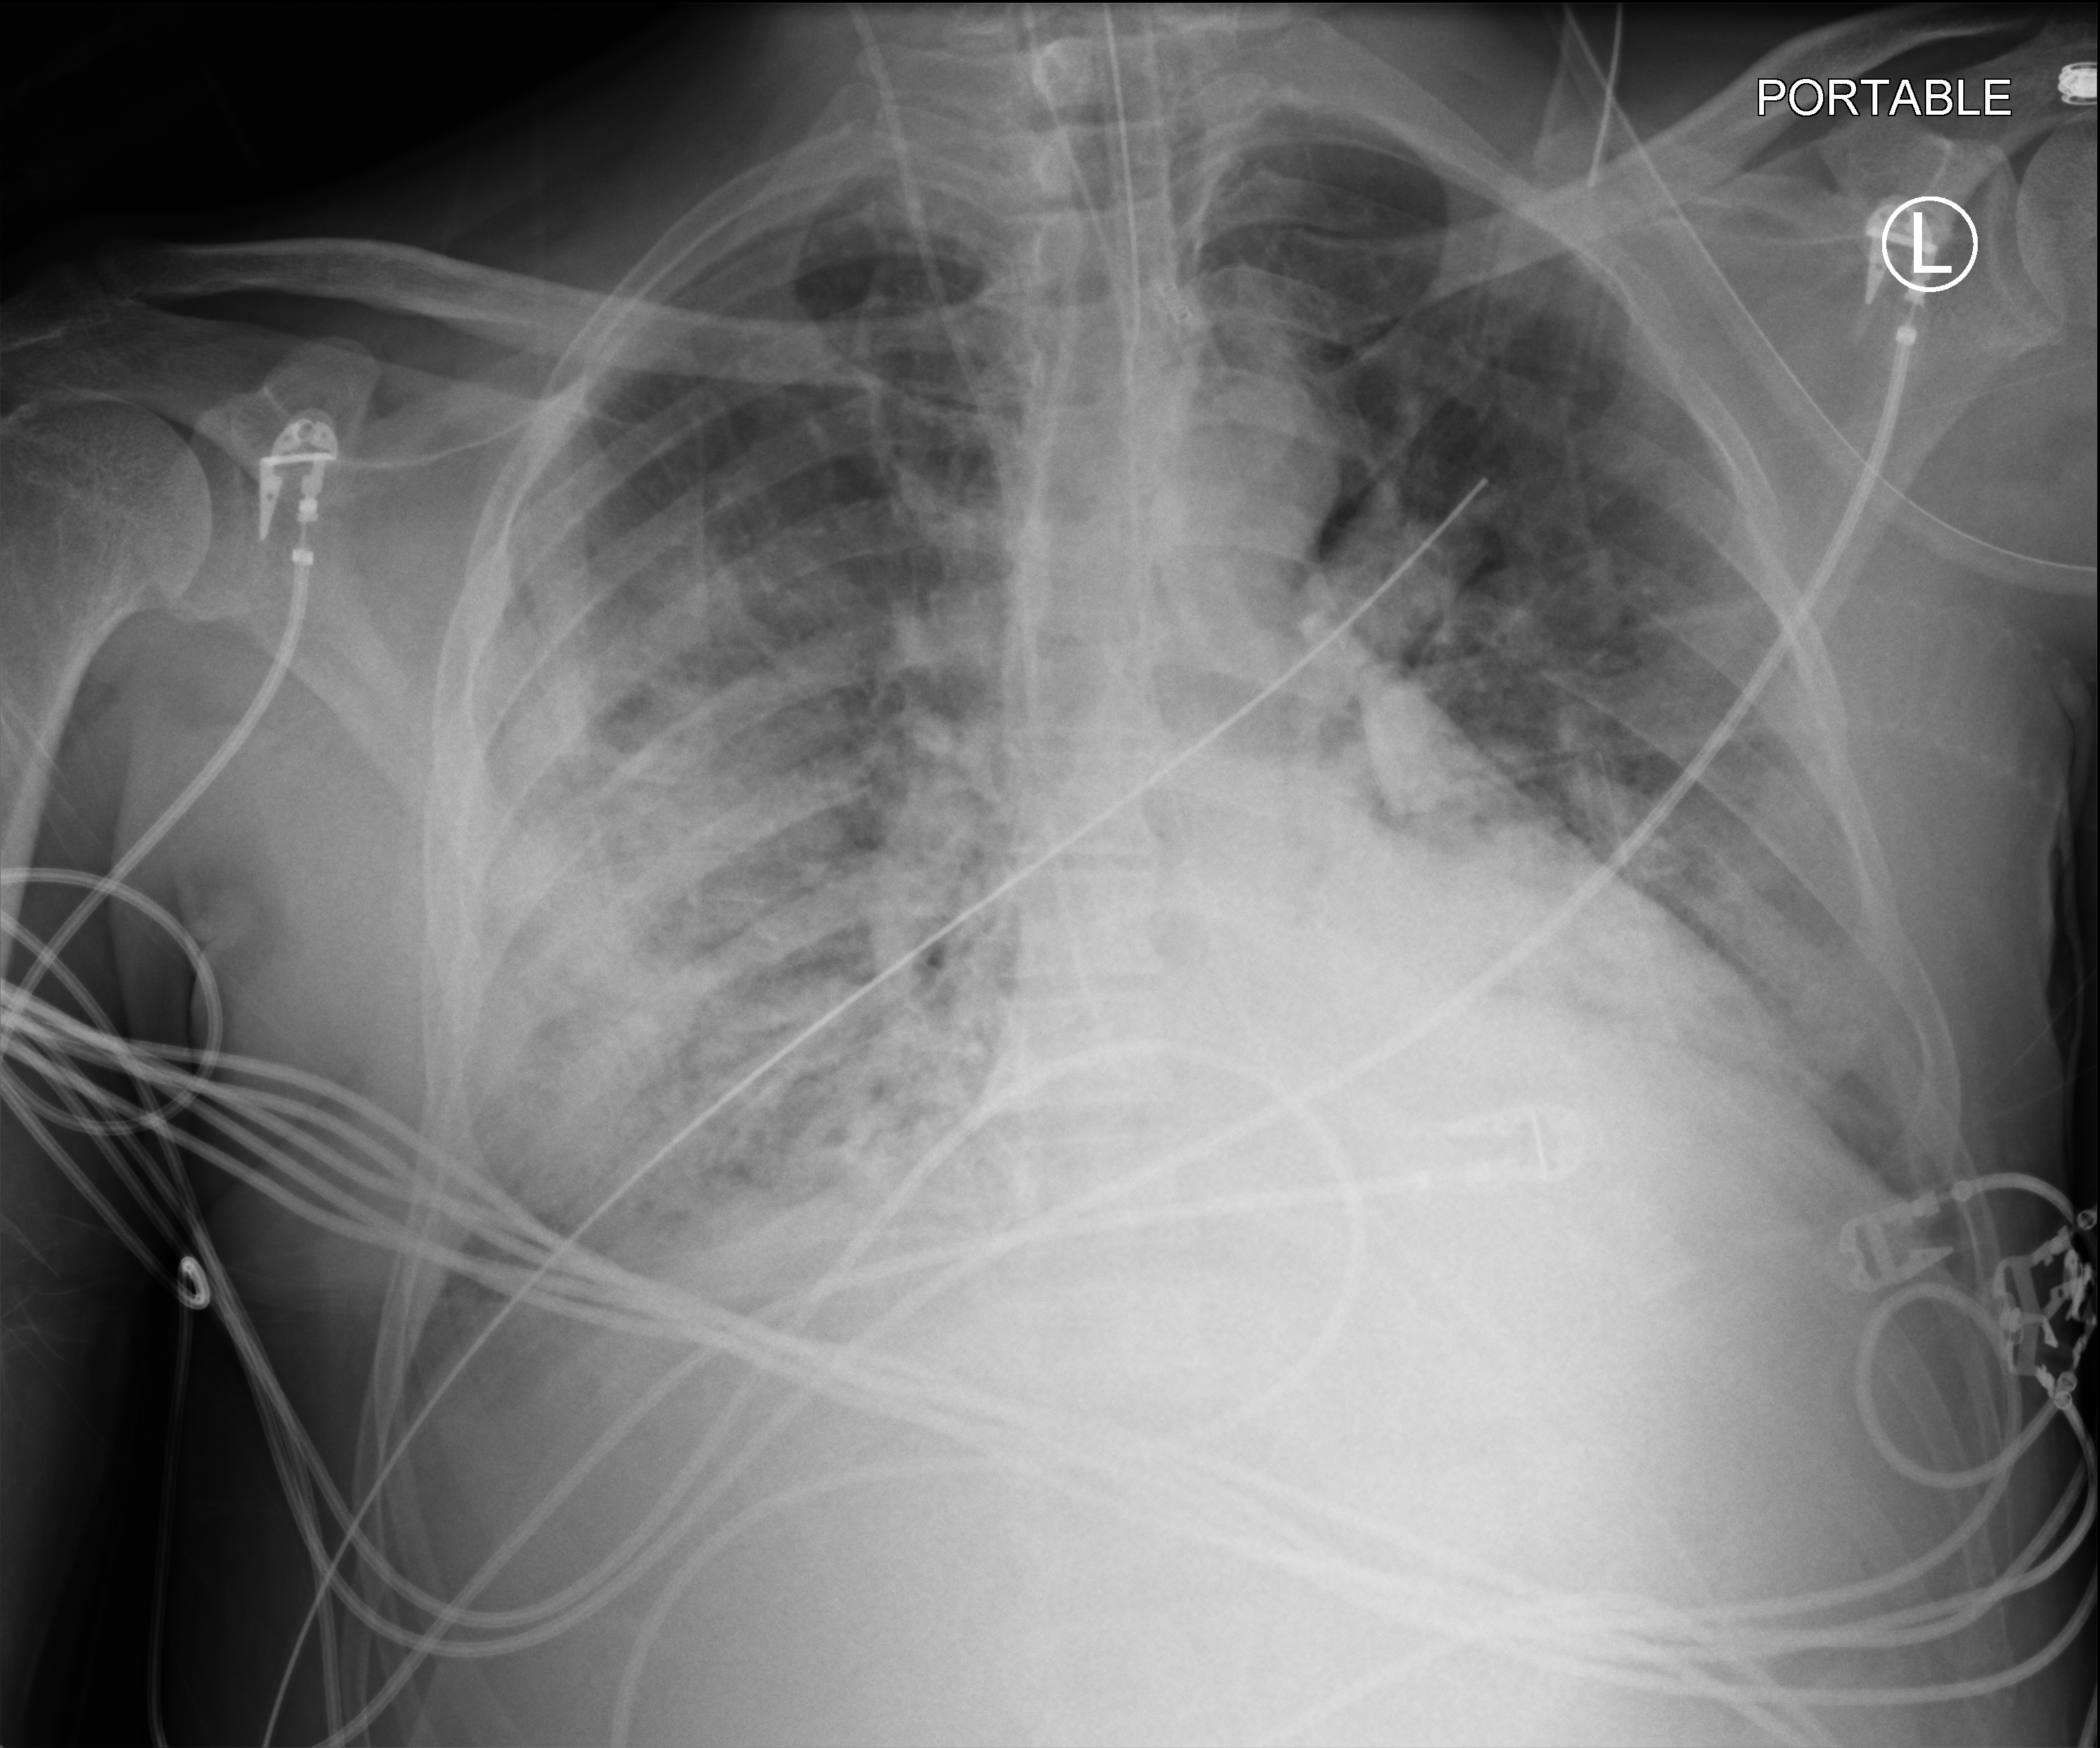
Bedside chest radiograph (computed radiography). Patient hospitalised with COVID-19; male, aged 18–59 years.
Admission-level facts for this patient (not findings on this image; timing relative to this image not recorded): admitted to intensive care during this hospital stay: yes; mechanically ventilated during this hospital stay: yes; length of hospital stay: 41 days.